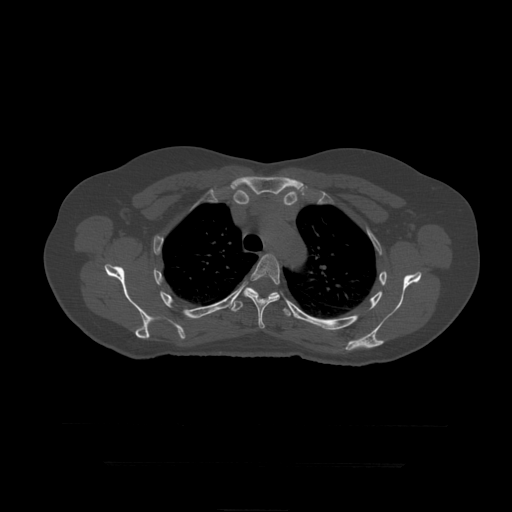
CT including the spine, one axial slice; slice 332 of 399 in the series (ordered by position); 120 kVp; bone window (W 1800 / L 400 HU); 512 × 512 image matrix, field of view 450 × 450 mm. Patient age 41 years. Case-level facts recorded for this patient, not image findings: primary cancer: breast.
Annotated regions visible in this slice (semi-automatically segmented with operator editing):
- T5 vertebra: box from (x=243, y=254) to (x=280, y=329) px
- T6 vertebra: (x=231, y=287)–(x=301, y=320)